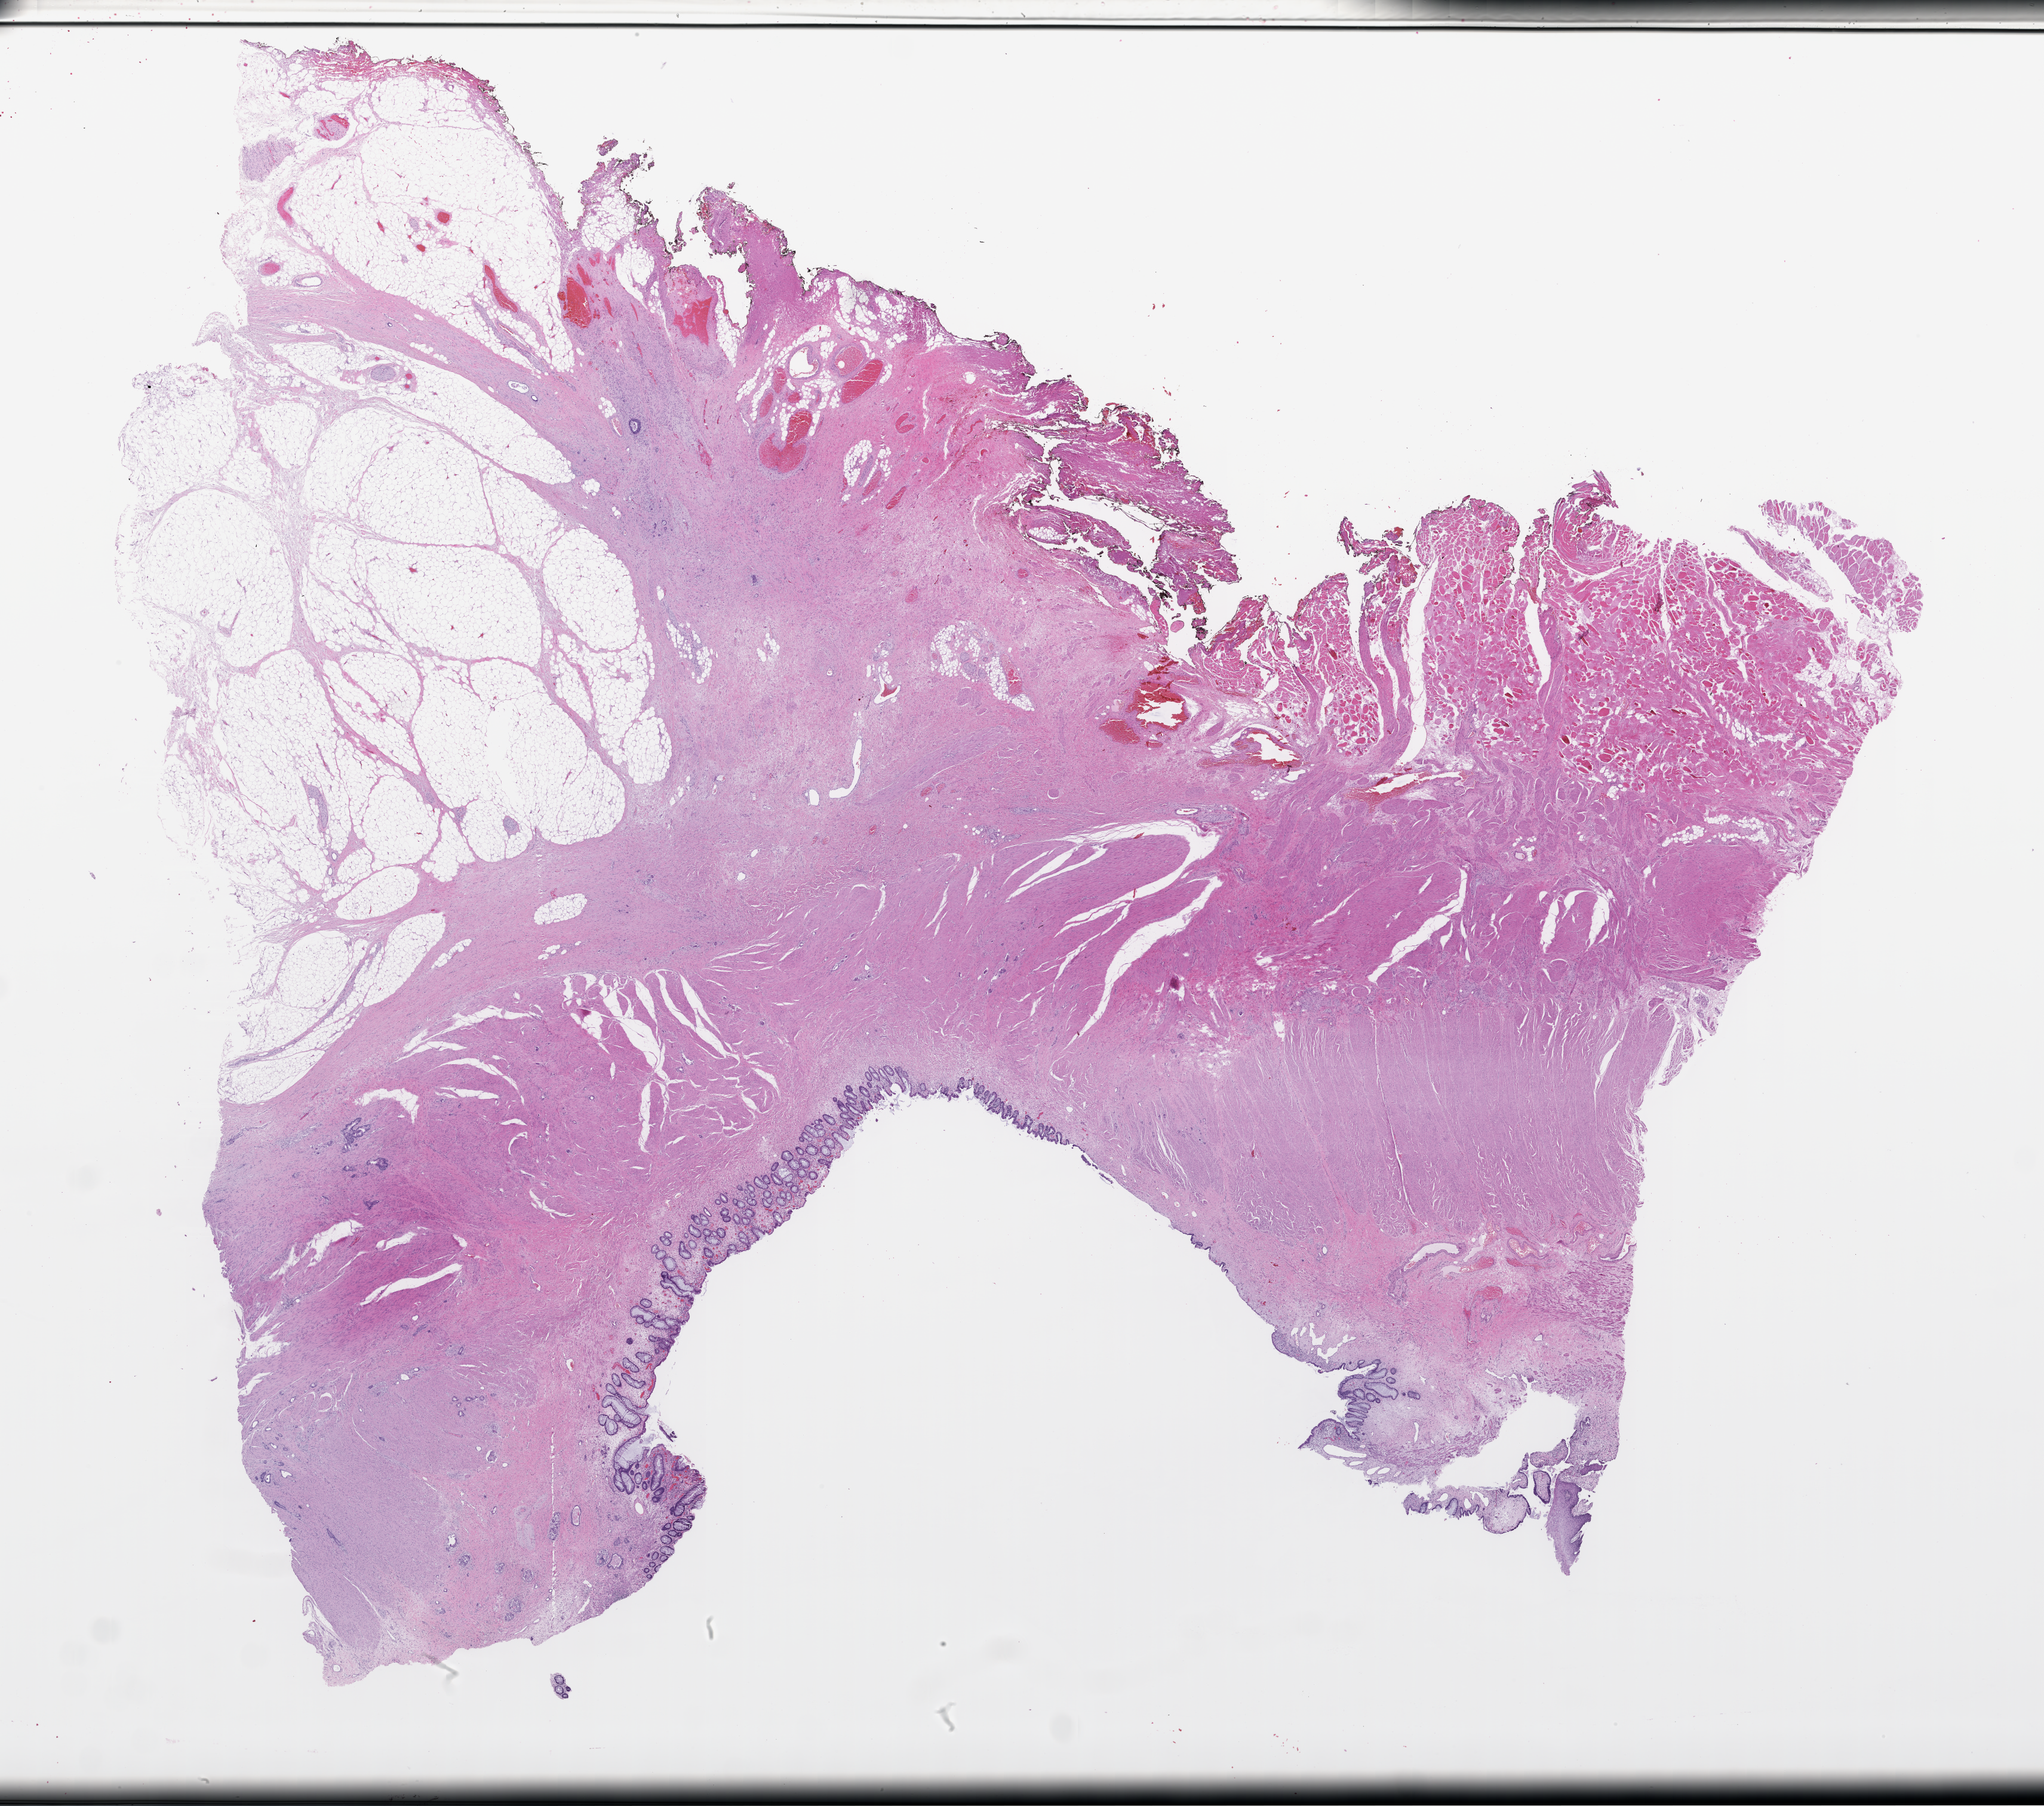
Whole-slide image, H&E stain — low-resolution overview of the scanned area, about 27.6 x 24.4 mm; formalin-fixed paraffin-embedded section; tissue site: rectum; specimen time point: archival tissue. Patient sex: male.
This section: primary tumour tissue. Diagnosis: Colorectal Carcinoma.